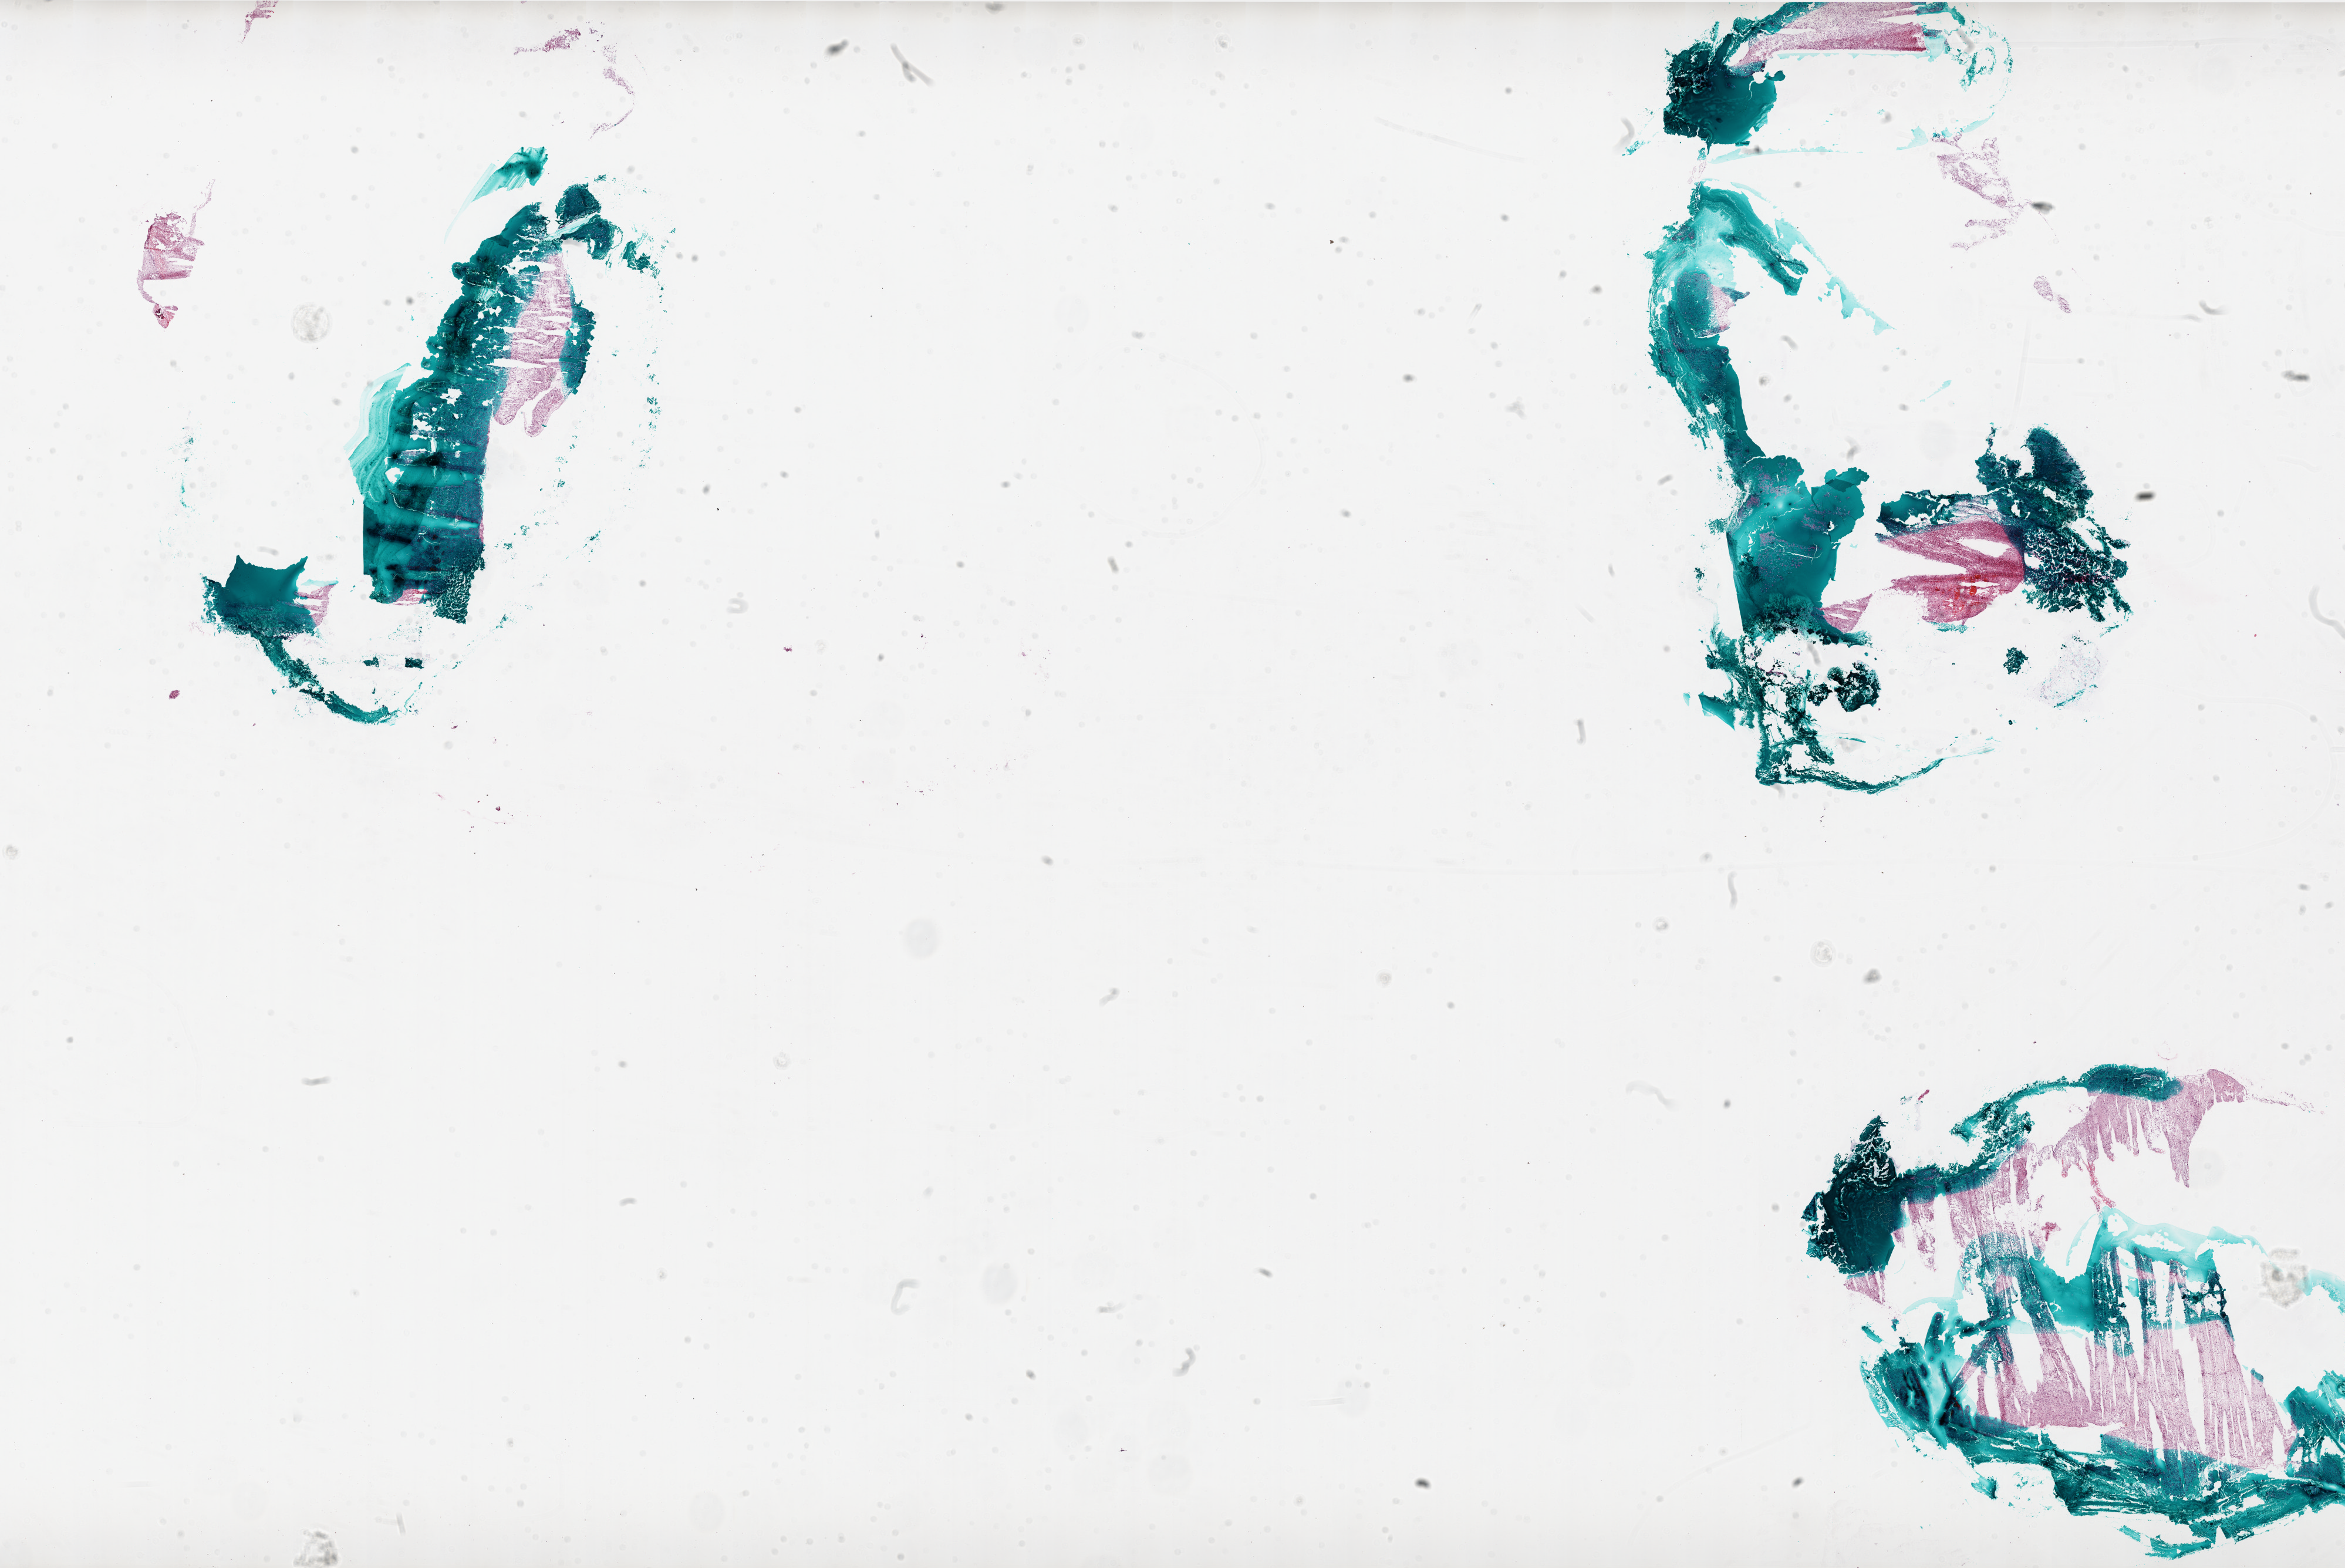
Digitized H&E-stained tissue section (whole slide), whole scanned area (about 32.0 x 21.4 mm, acquisition: 20x scan) shown as a low-resolution overview, frozen section from the bottom of the tissue portion, sample: primary tumour, brain. Patient: male, age at initial diagnosis 50 years. Composition of this section per pathologist review: tumour cells 100%, tumour nuclei 100%, normal cells 0%, stromal cells 0%, necrosis 0%.
Pathologic diagnosis: Glioblastoma.